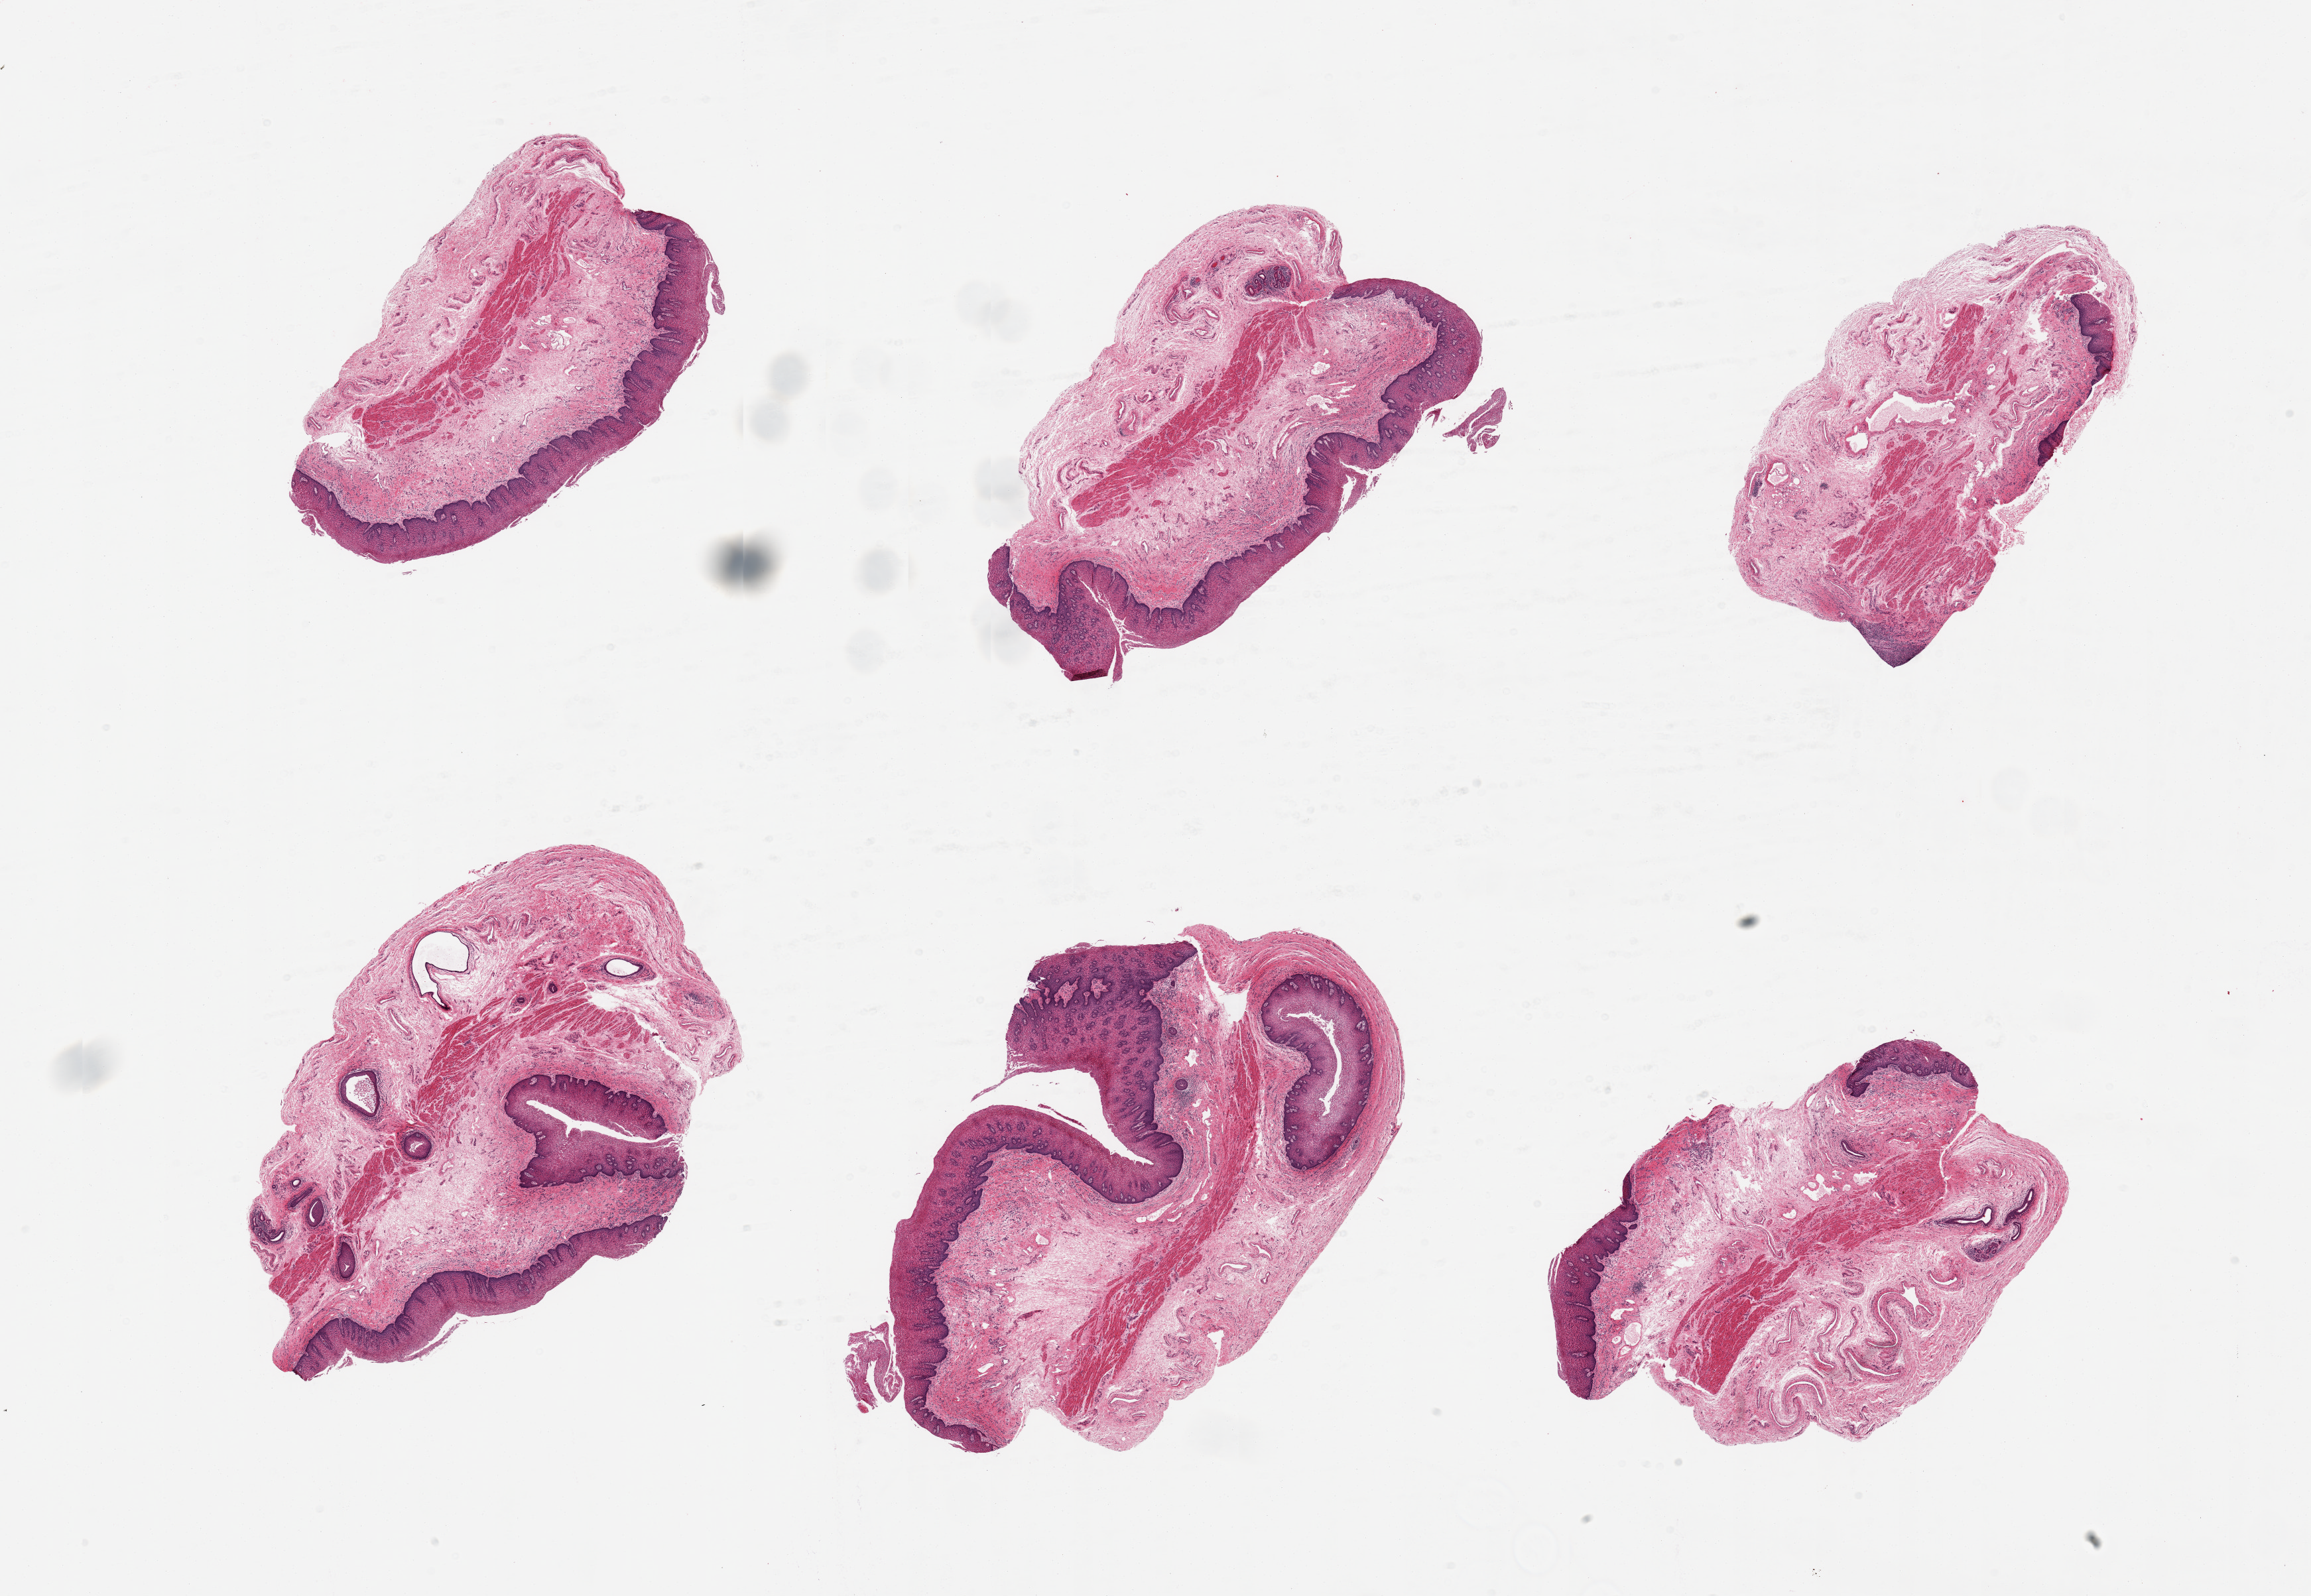
Whole-slide image, H&E stain, shown as a low-resolution overview of the whole scanned area (about 27.6 x 19.0 mm). PAXgene-fixed paraffin-embedded (PFPE) section. Target tissue: gastroesophageal junction. Tissue donor sample. Donor sex: female.
Pathologist's review note for this sample: 6 pieces; squamous mucosa sampled, not muscularis.